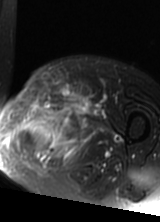
MRI of an extremity soft-tissue mass, one axial slice. Position 45 of 69 along the scan axis. T2-weighted fat-saturated. MR volume resampled by the dataset authors to the PET/CT grid (not the native acquisition matrix). 3.27 mm slice thickness. 160 × 222 image matrix, field of view 156 × 217 mm. Female patient. From the clinical record (not read from this slice): histological type: pleomorphic leiomyosarcoma; grade: high; site of the primary tumour: left thigh.
Annotated regions visible in this slice (expert contour drawn on MRI and transferred to this co-registered scan by the dataset authors):
- gross tumour volume including surrounding oedema: bounding box <16,88,92,162> (left, top, right, bottom; pixels)
- gross tumour volume (mass): <57,114,74,124>